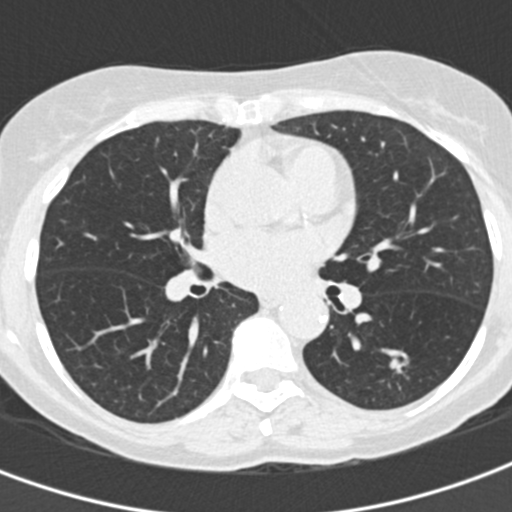
Low-dose screening chest CT, one axial slice. Slice 80 of 155 in the series (ordered by position). Reconstruction kernel B30f. Lung window (W 1500 / L -600 HU). 512 × 512 image matrix, field of view 282 × 282 mm.
Outlined on this slice (expert manual segmentation):
- lesion 1 (tumor, lower lobe of left lung): bounding box <389,353,409,374> (left, top, right, bottom; pixels)